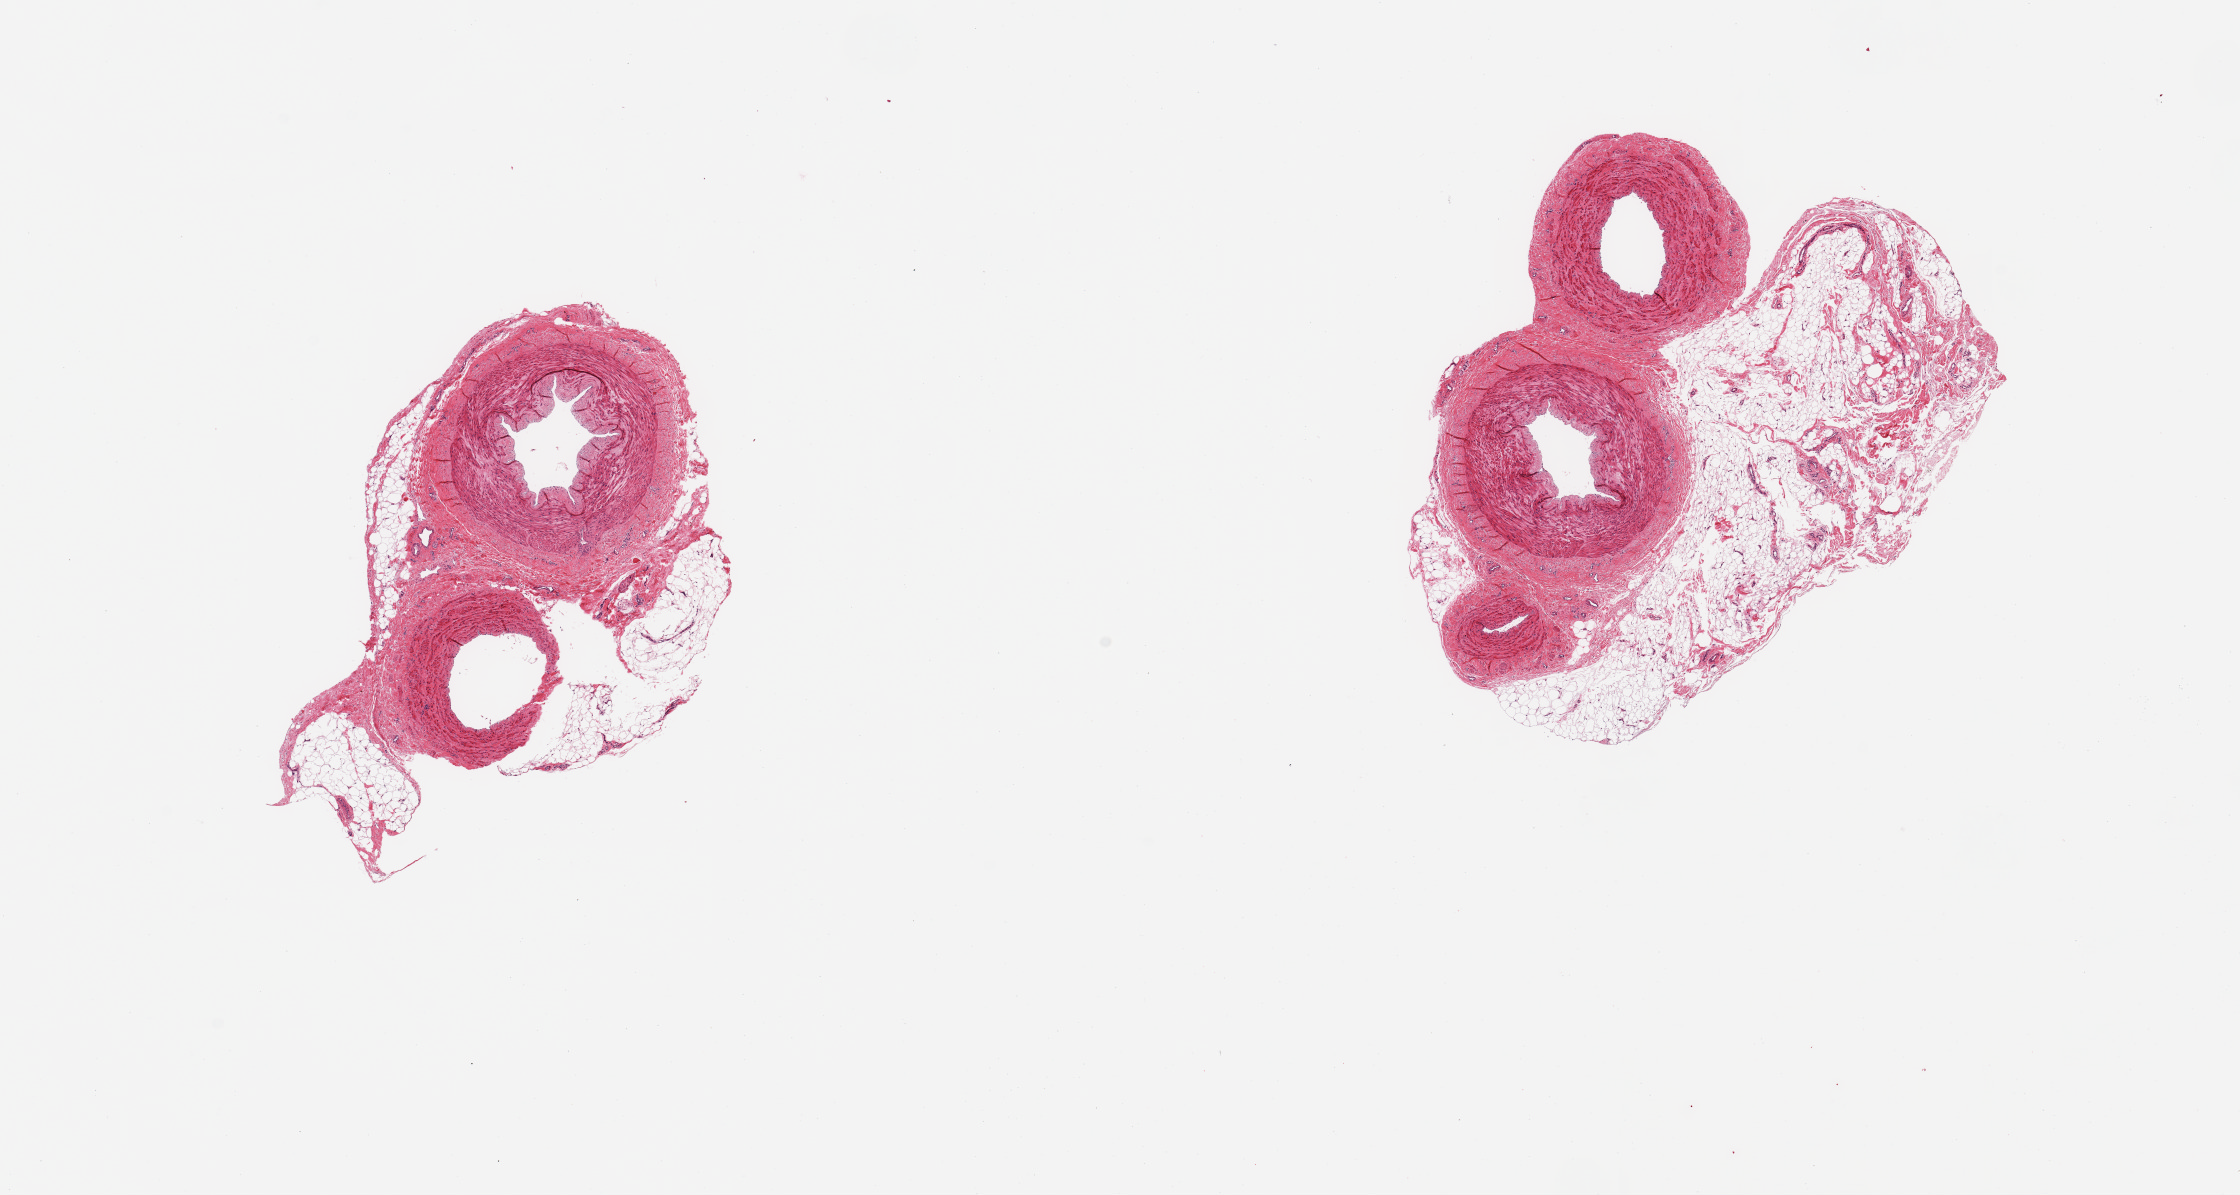
Whole-slide image, hematoxylin and eosin (H&E) stain — a low-resolution overview of the entire scanned area, about 17.7 x 9.5 mm (acquisition: 20x scan); PAXgene-fixed, paraffin-embedded tissue; sampled site (target tissue): tibial artery; donor tissue sample.
Pathologist's review note for this sample: 2 pieces, prominent nubbins of adherent fat/fibrous tissue up to ~5x2.5mm.